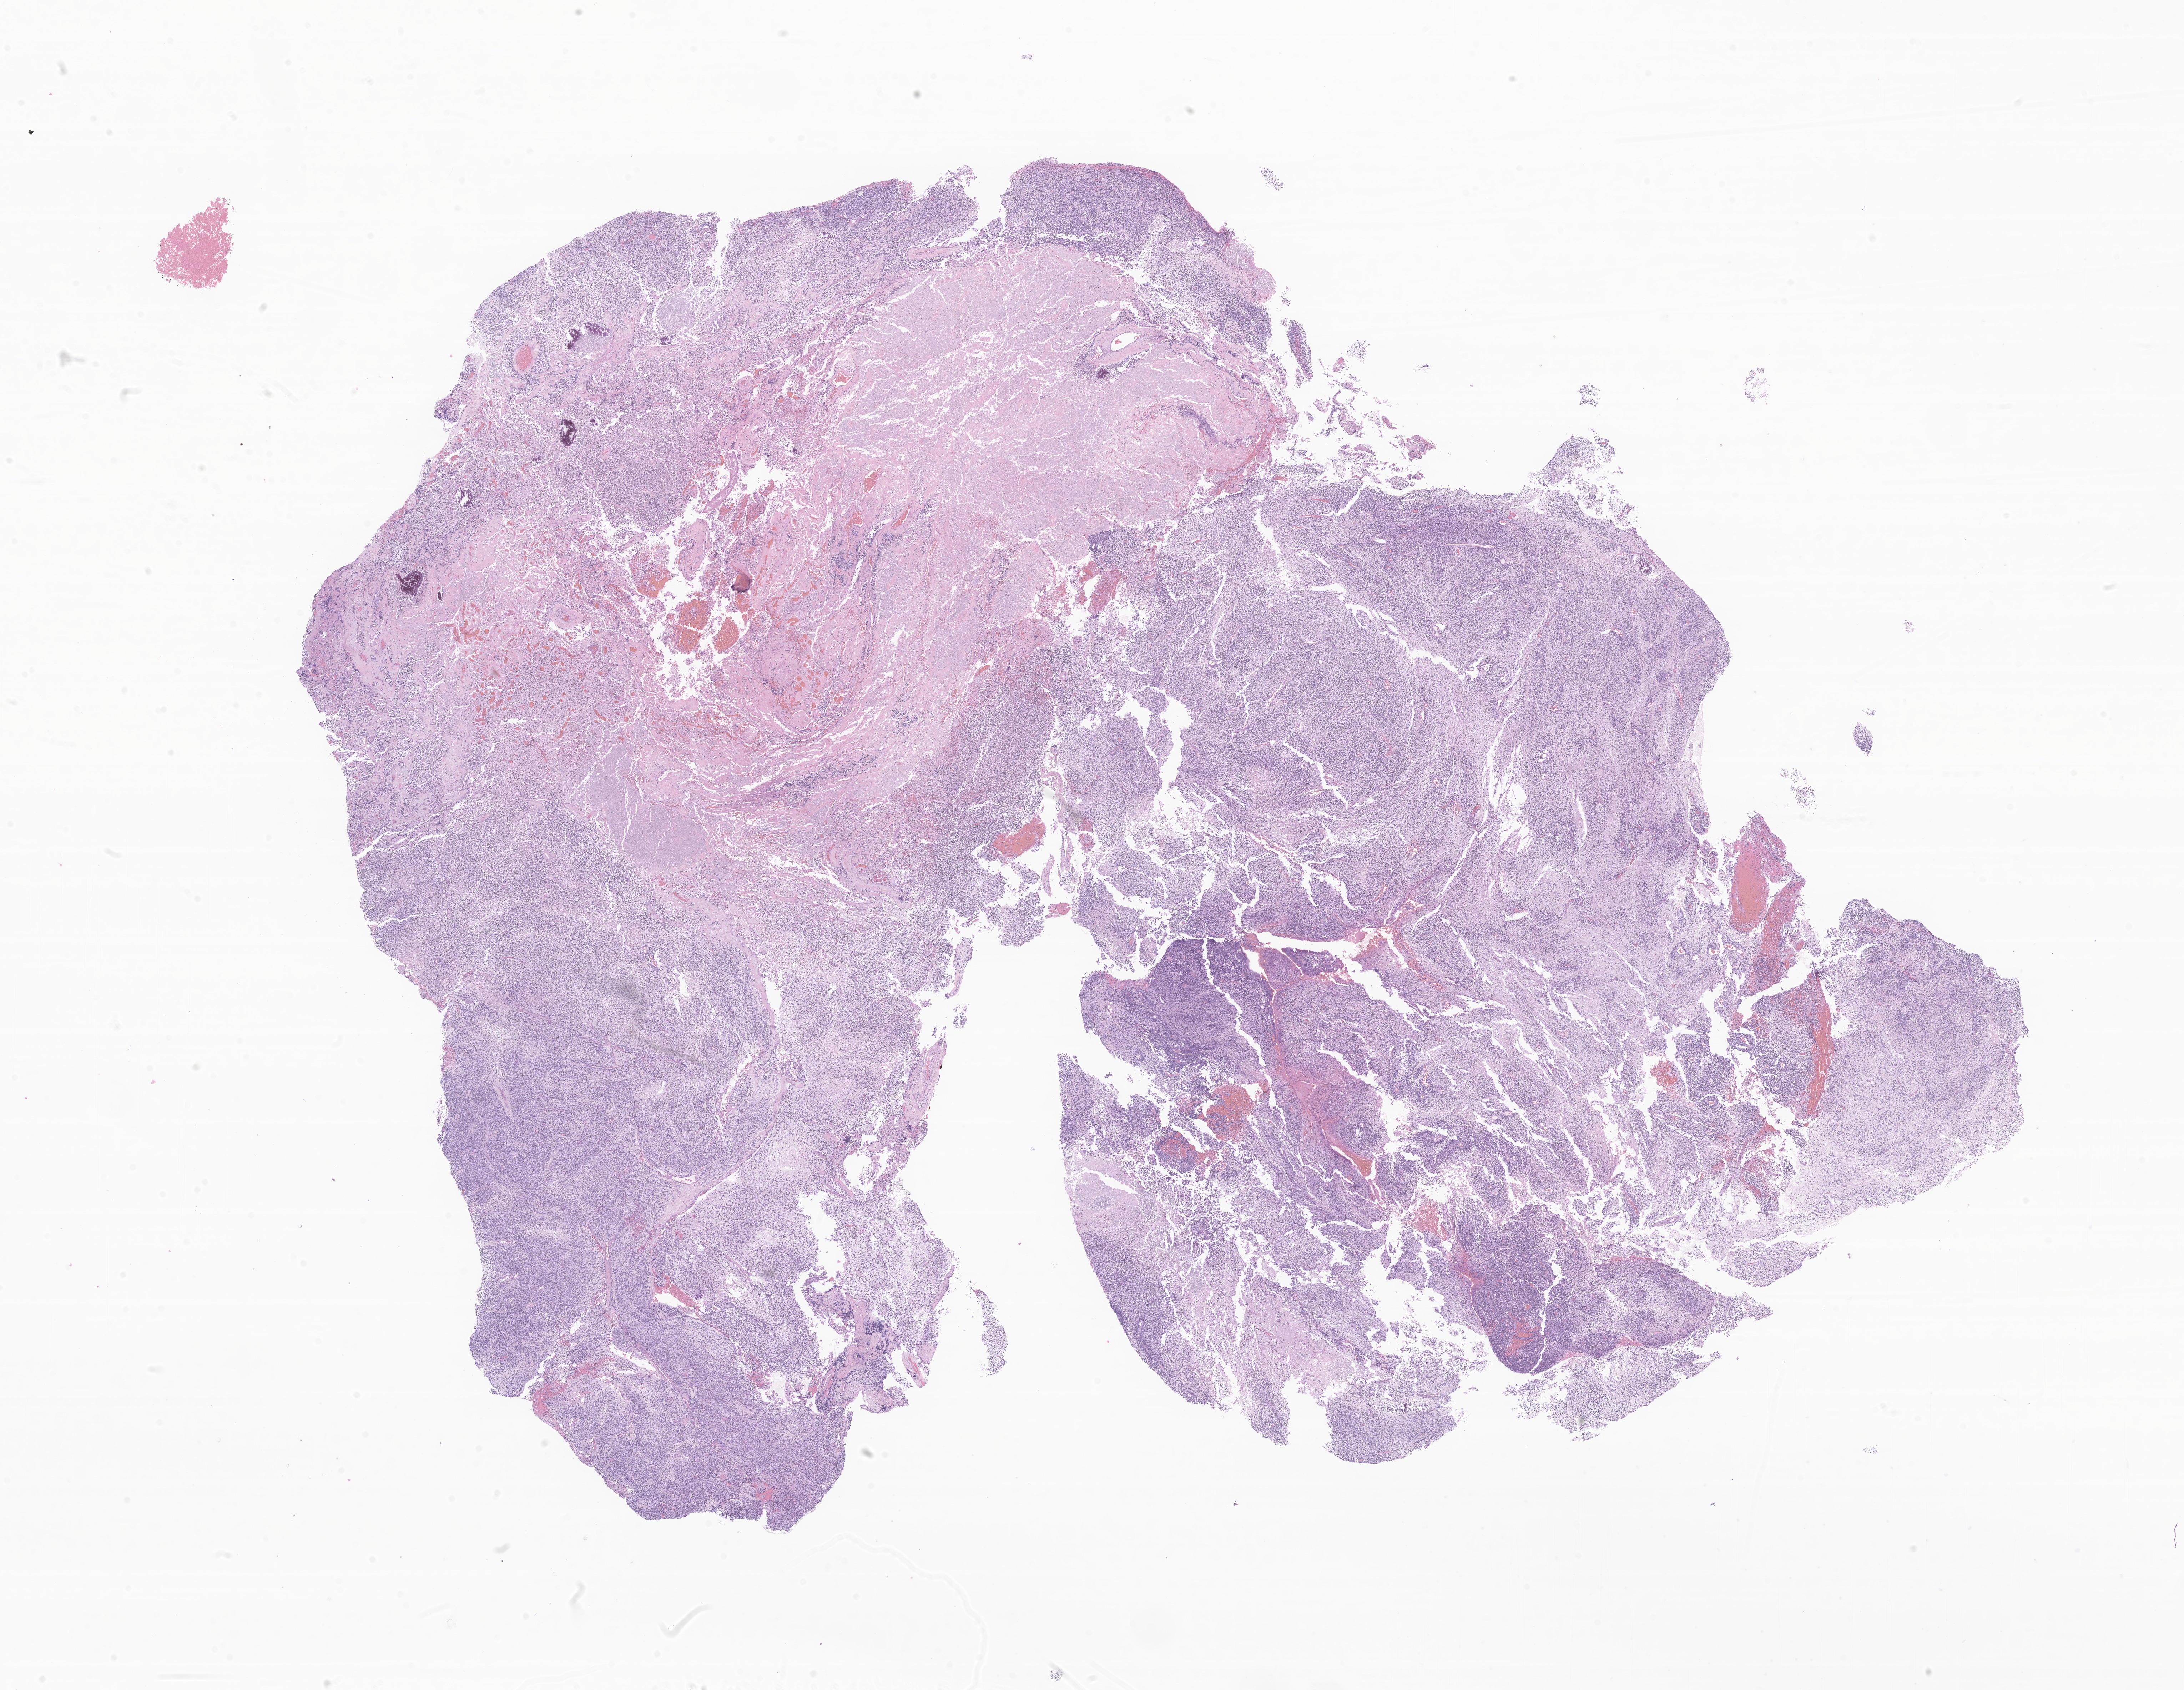
Whole-slide image, haematoxylin and eosin stain of tumor tissue from the parietal lobe — low-resolution overview of the scanned area, about 25.8 x 20.0 mm. Formalin-fixed paraffin-embedded section. Patient: female, age 43 months (3 years 7 months).
Diagnosis (ICD-O-3 morphology term): Embryonal carcinoma, NOS.